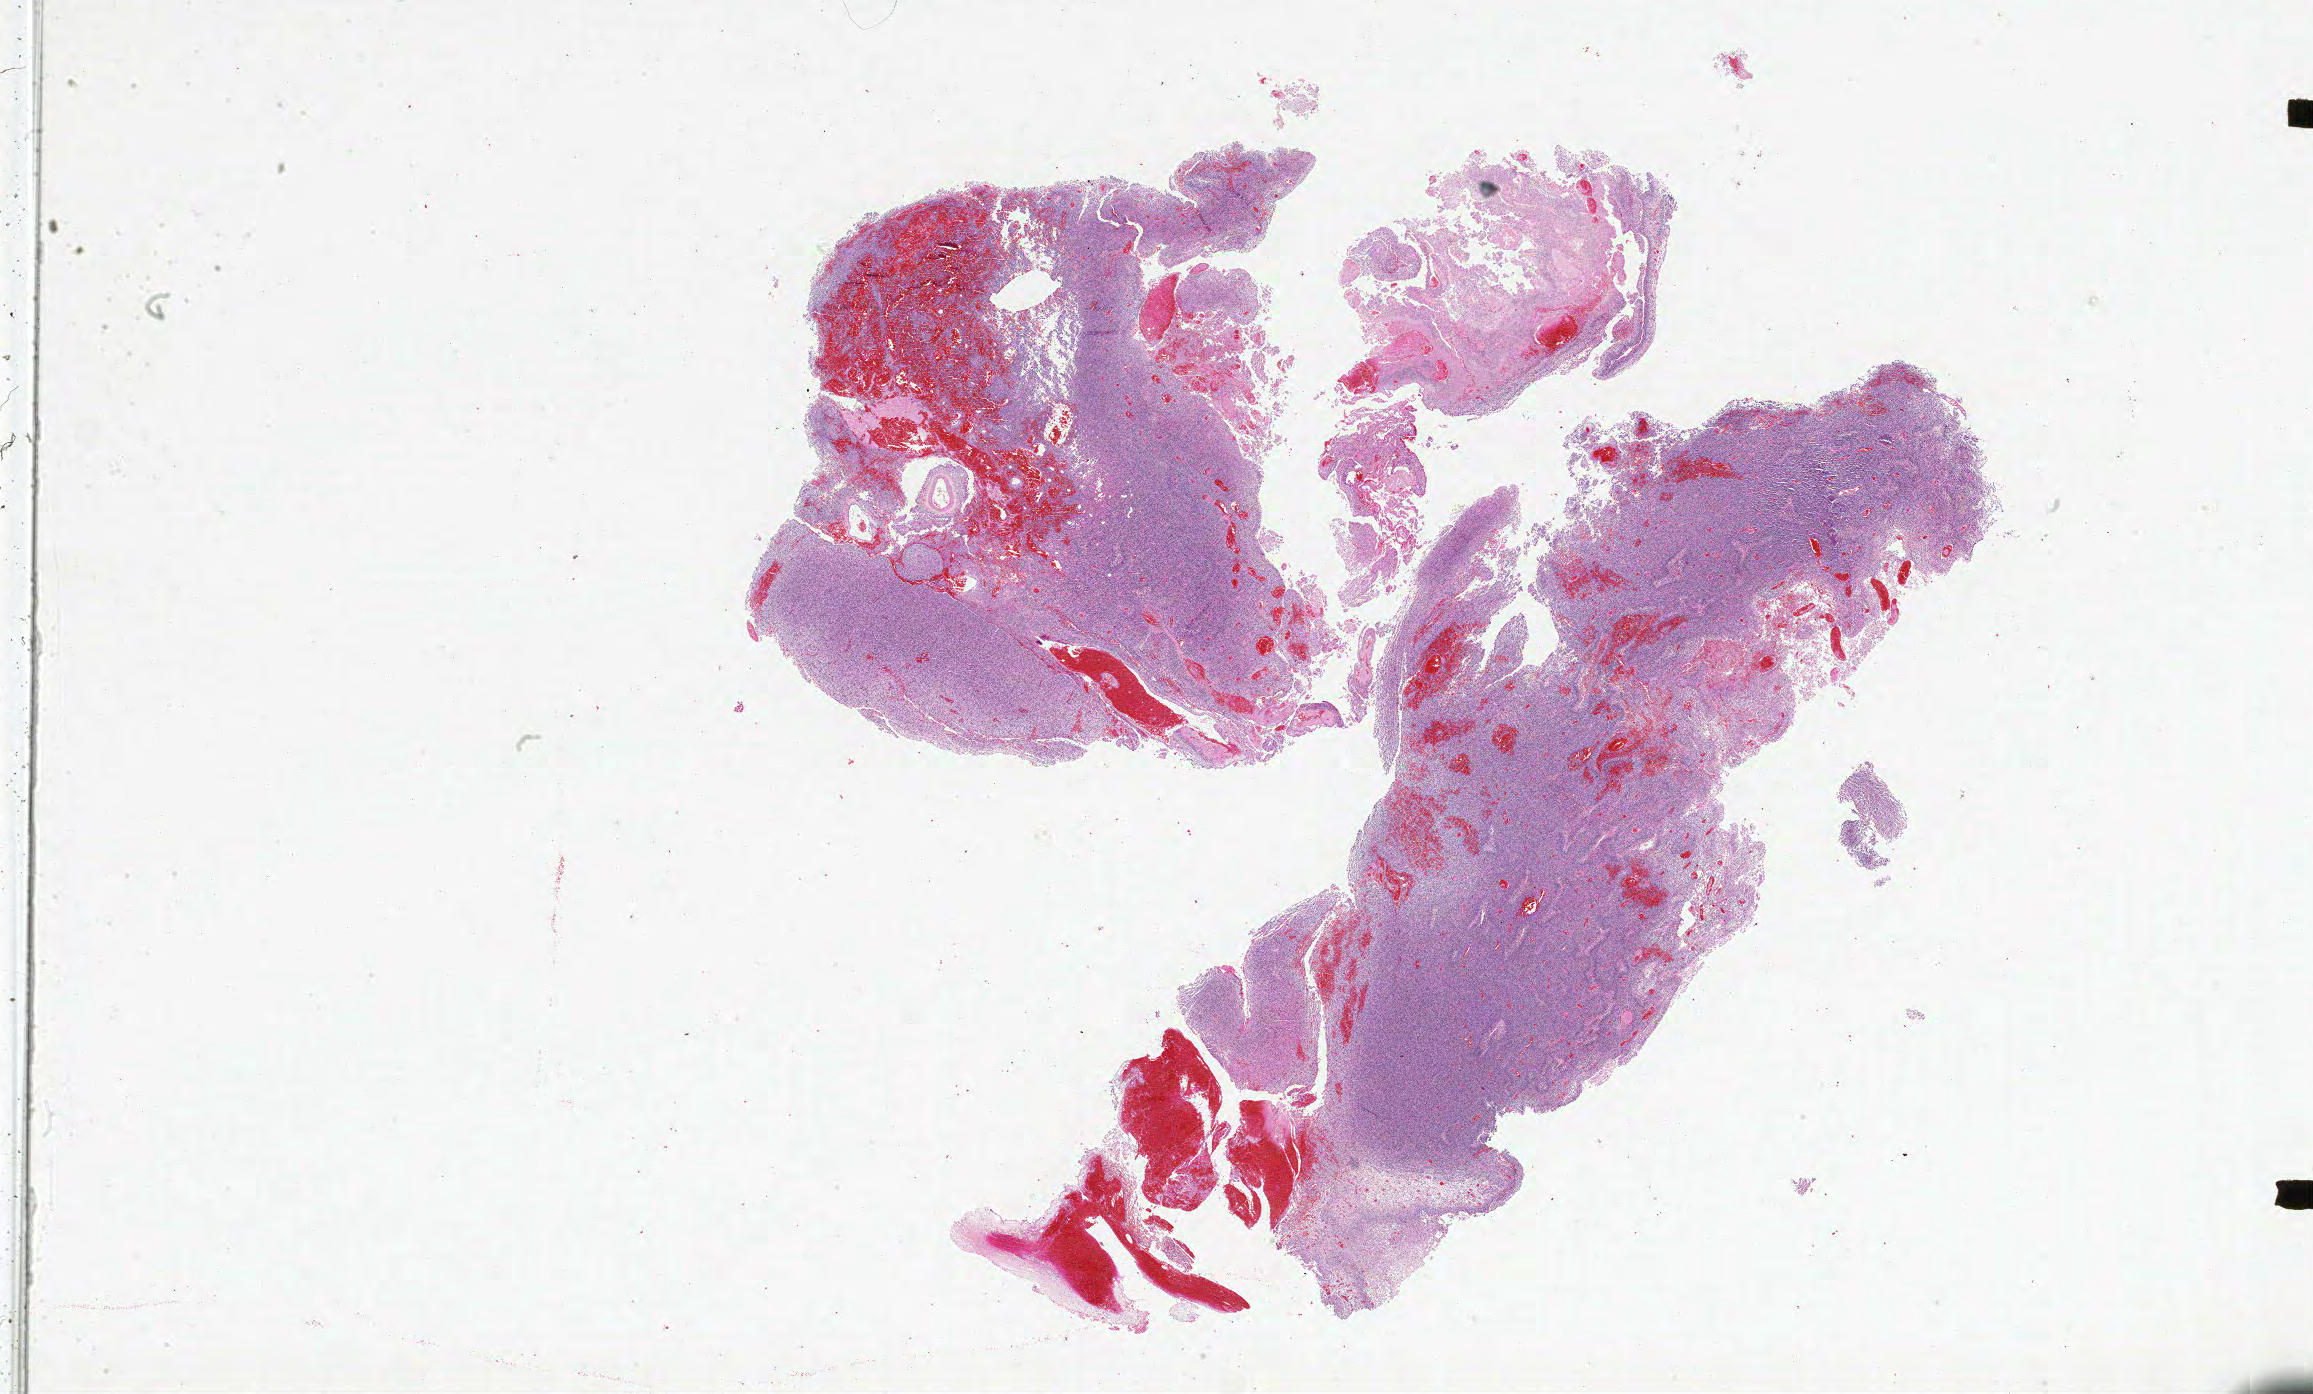
H&E-stained whole-slide image, low-resolution overview of the scanned area, about 37.0 x 22.3 mm (from a 20x scan), formalin-fixed paraffin-embedded (FFPE) diagnostic section, primary tumour sample from the brain. Female patient; age at initial diagnosis 10 years.
- diagnosis: Glioblastoma